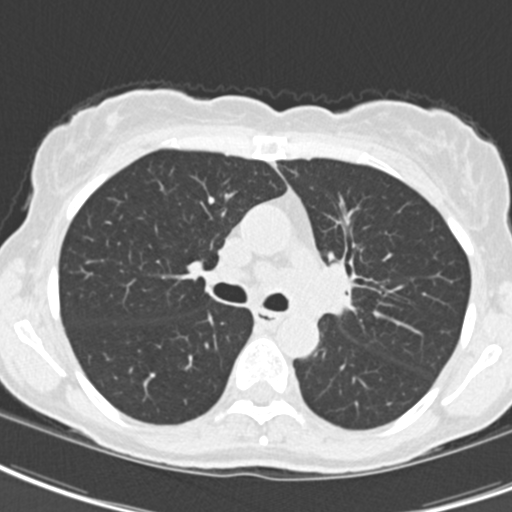
Low-dose screening chest CT, one axial slice; position 127 of 189 along the scan axis; 120 kVp; lung window (W 1500 / L -600 HU); 2 mm slice thickness; 512 × 512 image matrix, field of view 279 × 279 mm.
Outlined on this slice (expert manual segmentation):
- lesion 2 (tumor, hilum of left lung): box from (x=319, y=264) to (x=351, y=313) px